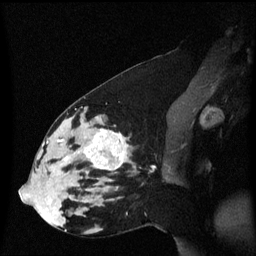
Breast MRI (dynamic contrast-enhanced), one sagittal slice; position 28 of 60 along the scan axis; dynamic contrast-enhanced series, image 2 of 3 at this slice position (ordered by acquisition); 1.5 T; TE 4.2 ms, TR 8.4 ms; 2 mm slice thickness; 256 × 256 image matrix, field of view 210 × 210 mm. Patient: female, 33 years. Case-level facts recorded for this patient, not image findings: setting: breast cancer imaged before/during neoadjuvant chemotherapy; receptor status: triple-negative.
Outlined on this slice (semi-automatic segmentation, software-assisted and operator-edited):
- analysis volume of interest (the breast-tissue region the enhancement analysis was run in; not a lesion): bounding box (x1, y1, x2, y2) in pixels: (44, 123, 137, 189)
- tumour enhancement mask (voxels above the 70 % enhancement threshold inside the analysis volume of interest): (58, 130, 129, 170)